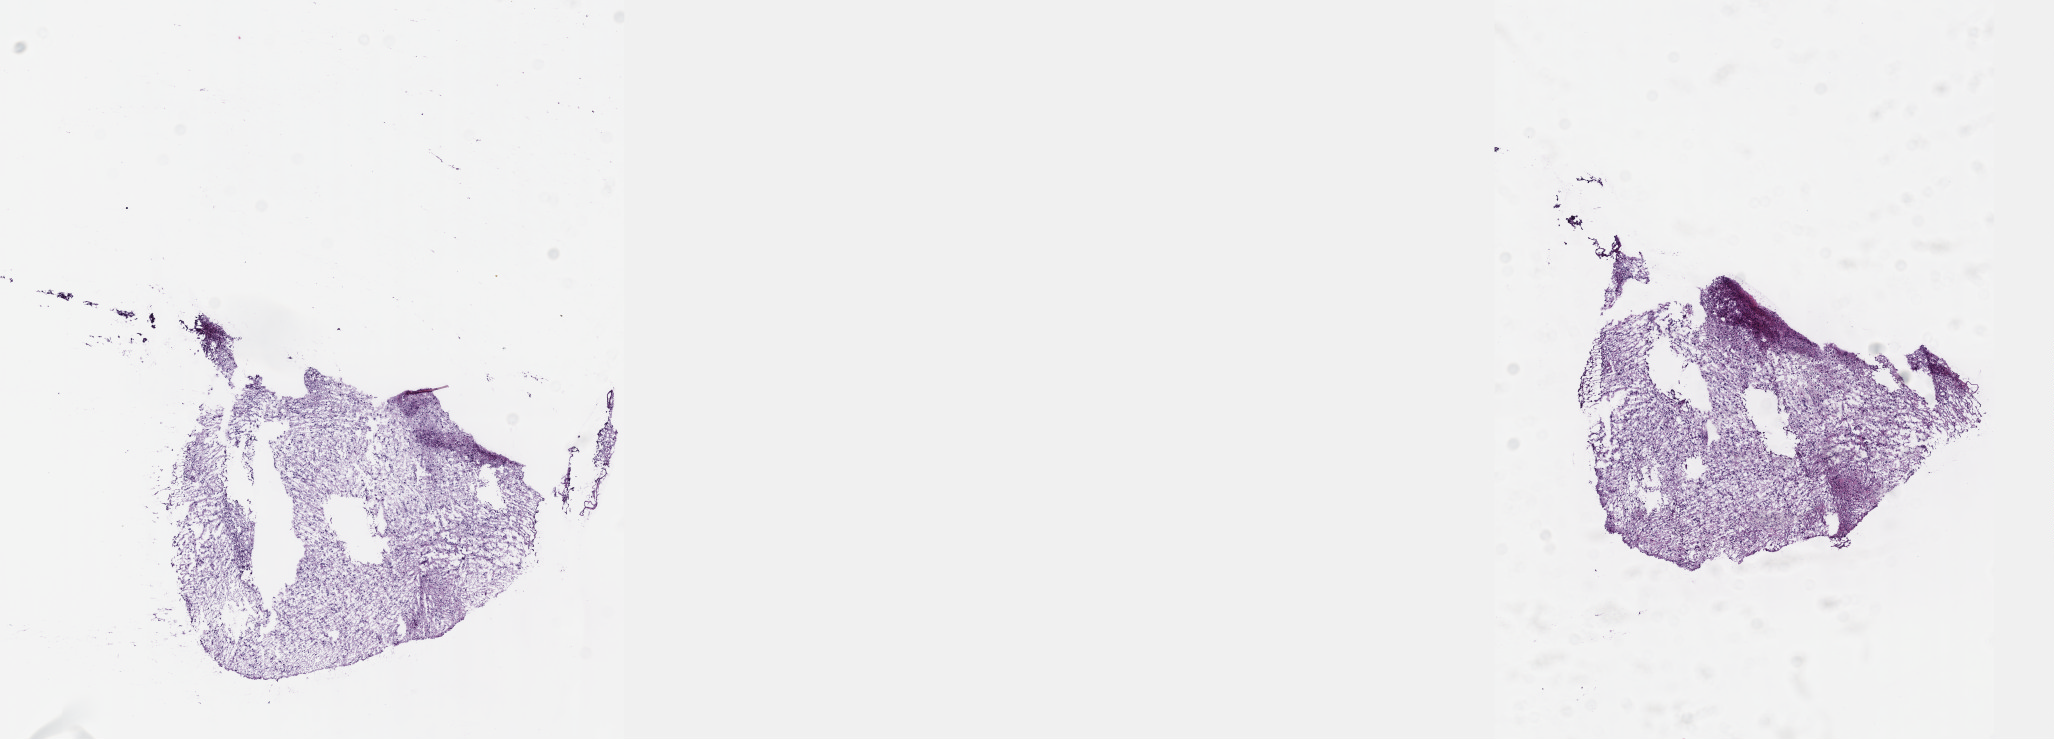
Whole-slide histology image, Hematoxylin and eosin (H&E) stained, whole scanned area (about 16.6 x 6.0 mm) shown as a low-resolution overview, frozen section, brain, recurrent tumour sample. Patient: male, age at initial diagnosis 29 years. Pathologist review of this section (percent, as recorded): tumour cells 40%, tumour nuclei 80%, normal cells 10%, stromal cells 50%, necrosis 0%. Inflammatory infiltration, as recorded: lymphocyte infiltration 0%, monocyte infiltration 0%, neutrophil infiltration 0%.
This section: recurrent tumour. Patient diagnosis: Oligodendroglioma, NOS (cerebrum).